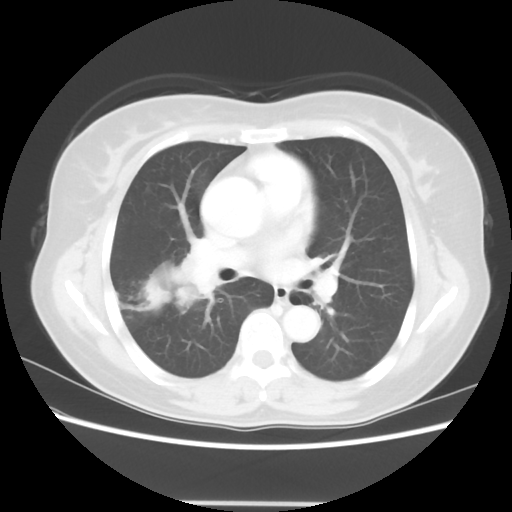
Chest CT, one axial slice; slice 33 of 56 in the series (ordered by position); reconstruction kernel STANDARD; 120 kVp; lung window (W 1500 / L -600 HU); 5 mm slice thickness; 512 × 512 image matrix, field of view 360 × 360 mm. Patient: female, 55 years. From the clinical record (not read from this slice): clinical TNM (as recorded): T2 N1 M0.
Structures marked on this image (bounding box drawn by a radiologist):
- lung tumour (recorded histology: adenocarcinoma): bounding box <117,247,231,333> (left, top, right, bottom; pixels)